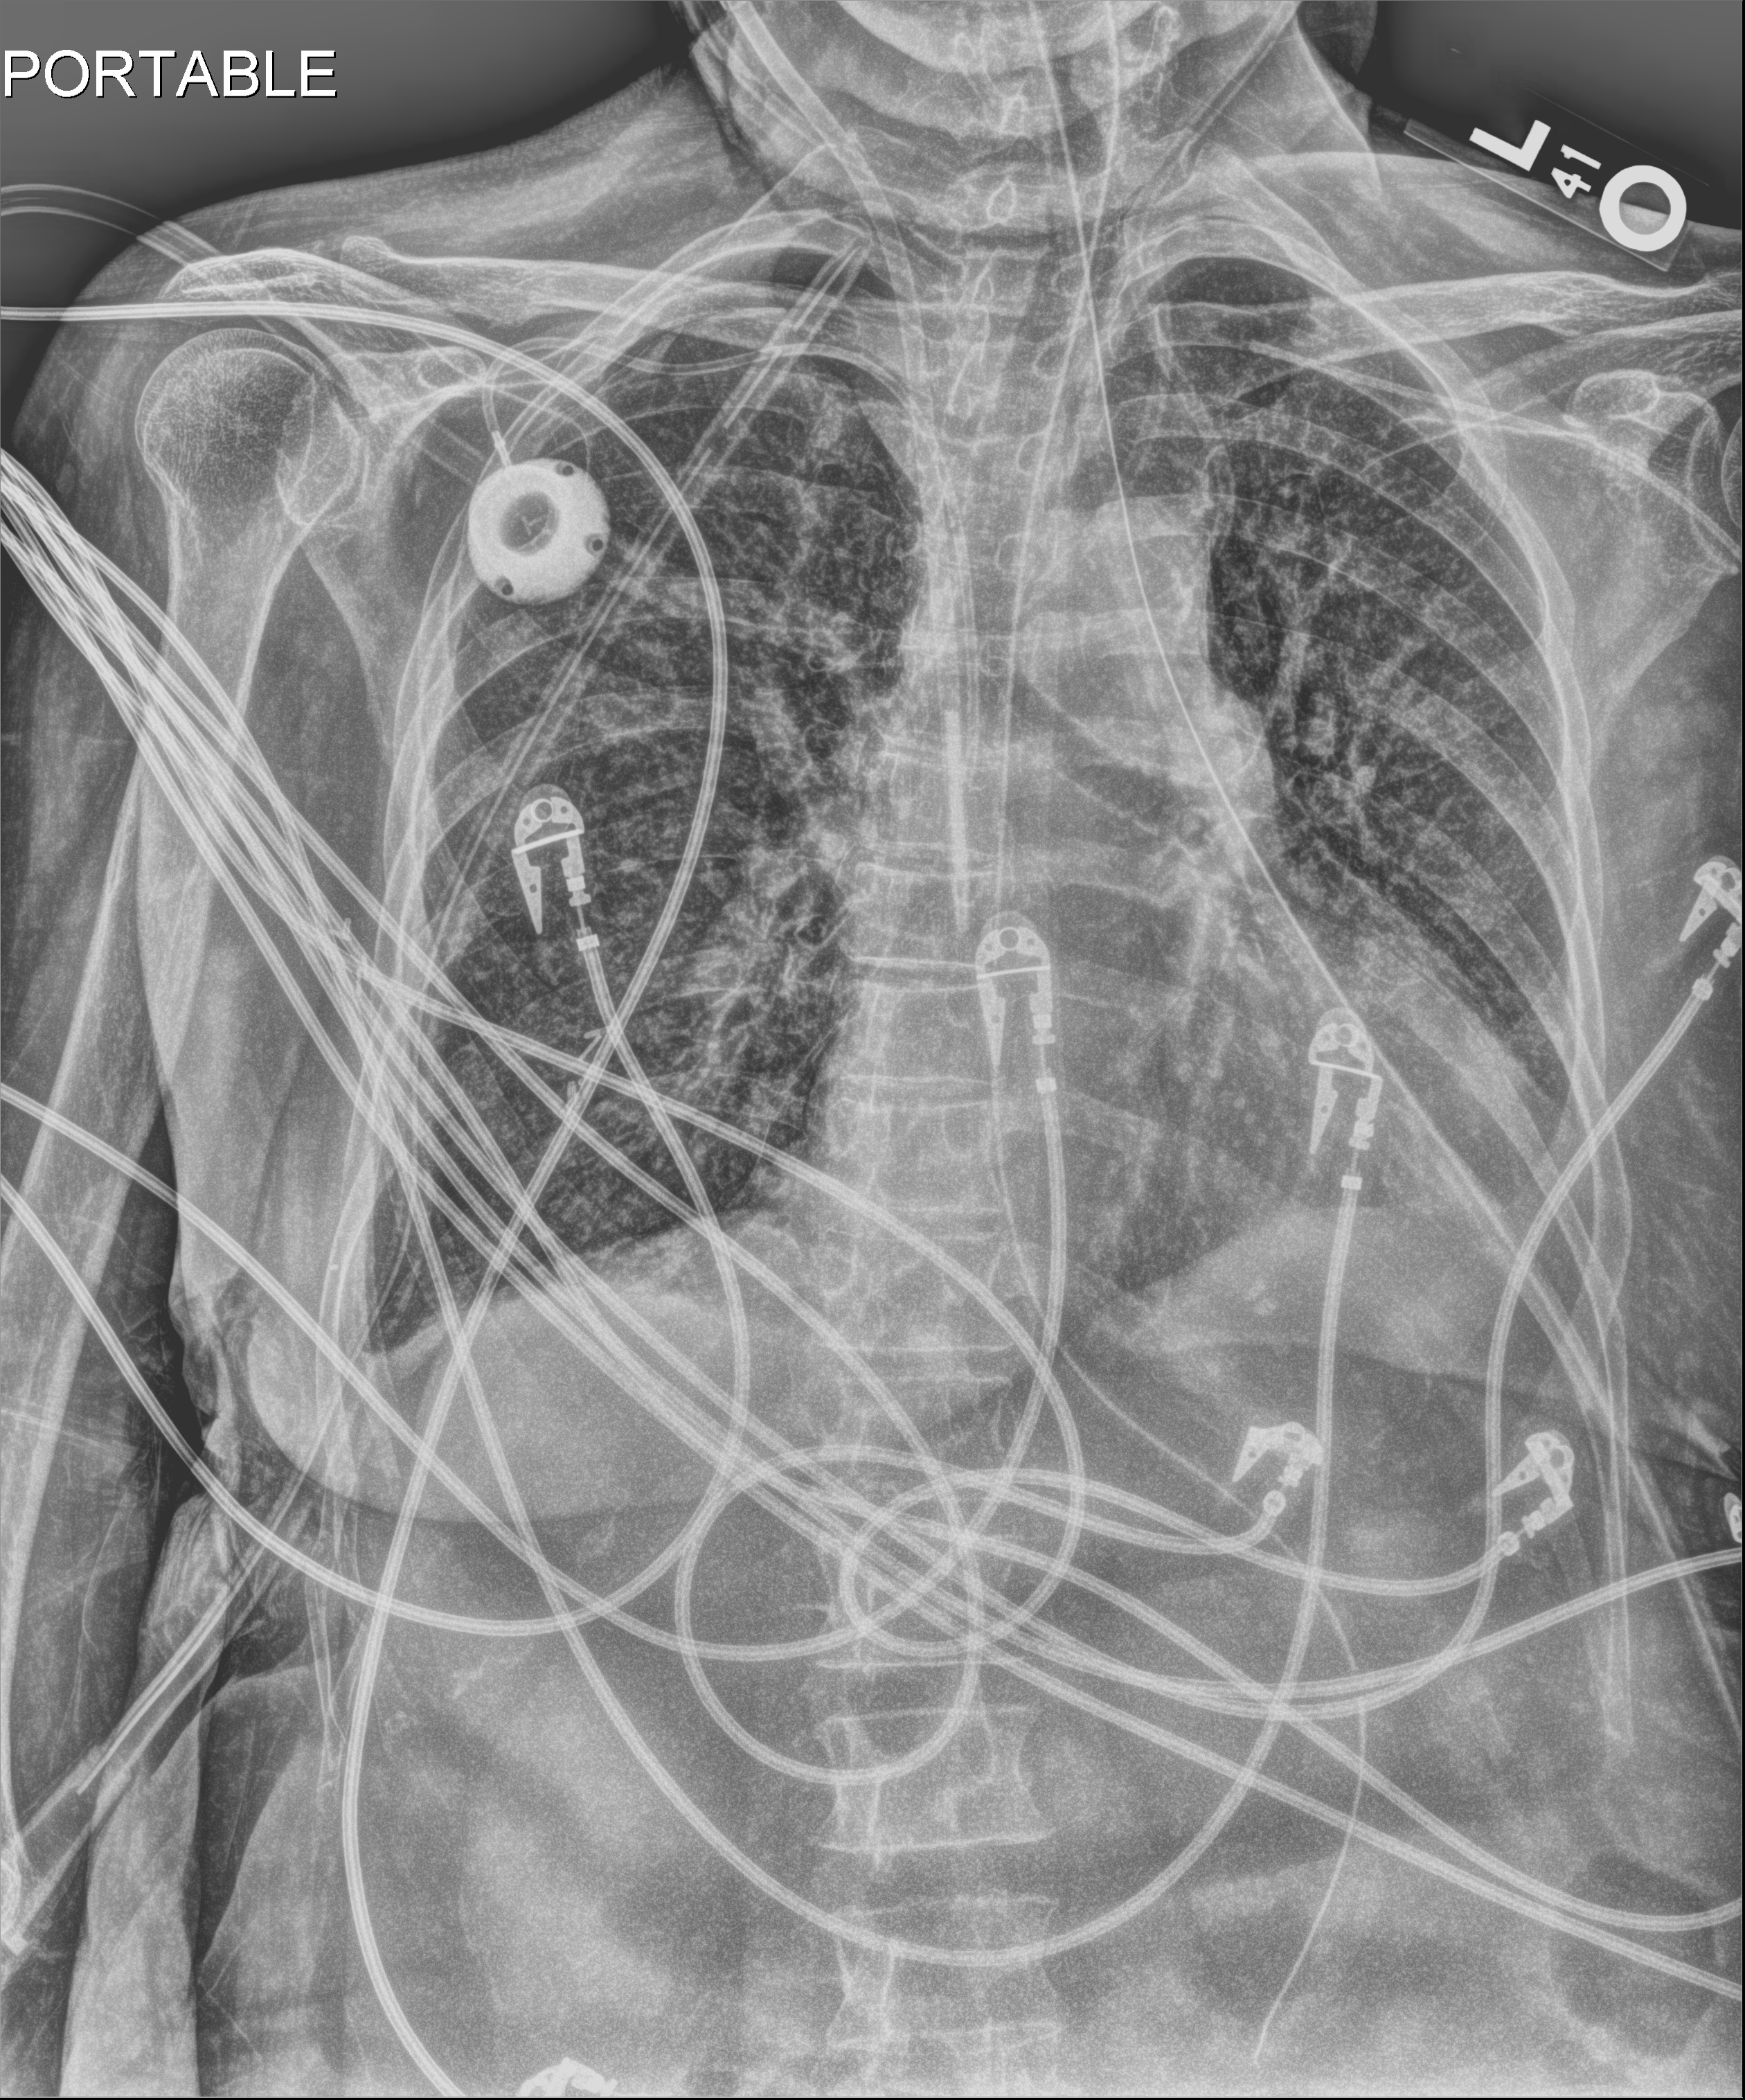
Chest radiograph (digital radiography). Patient hospitalised with COVID-19; female, aged 60–74 years.
Admission-level facts for this patient (not findings on this image; timing relative to this image not recorded):
- chronic kidney disease (admission record): no
- admitted to intensive care during this hospital stay: yes
- mechanically ventilated during this hospital stay: yes